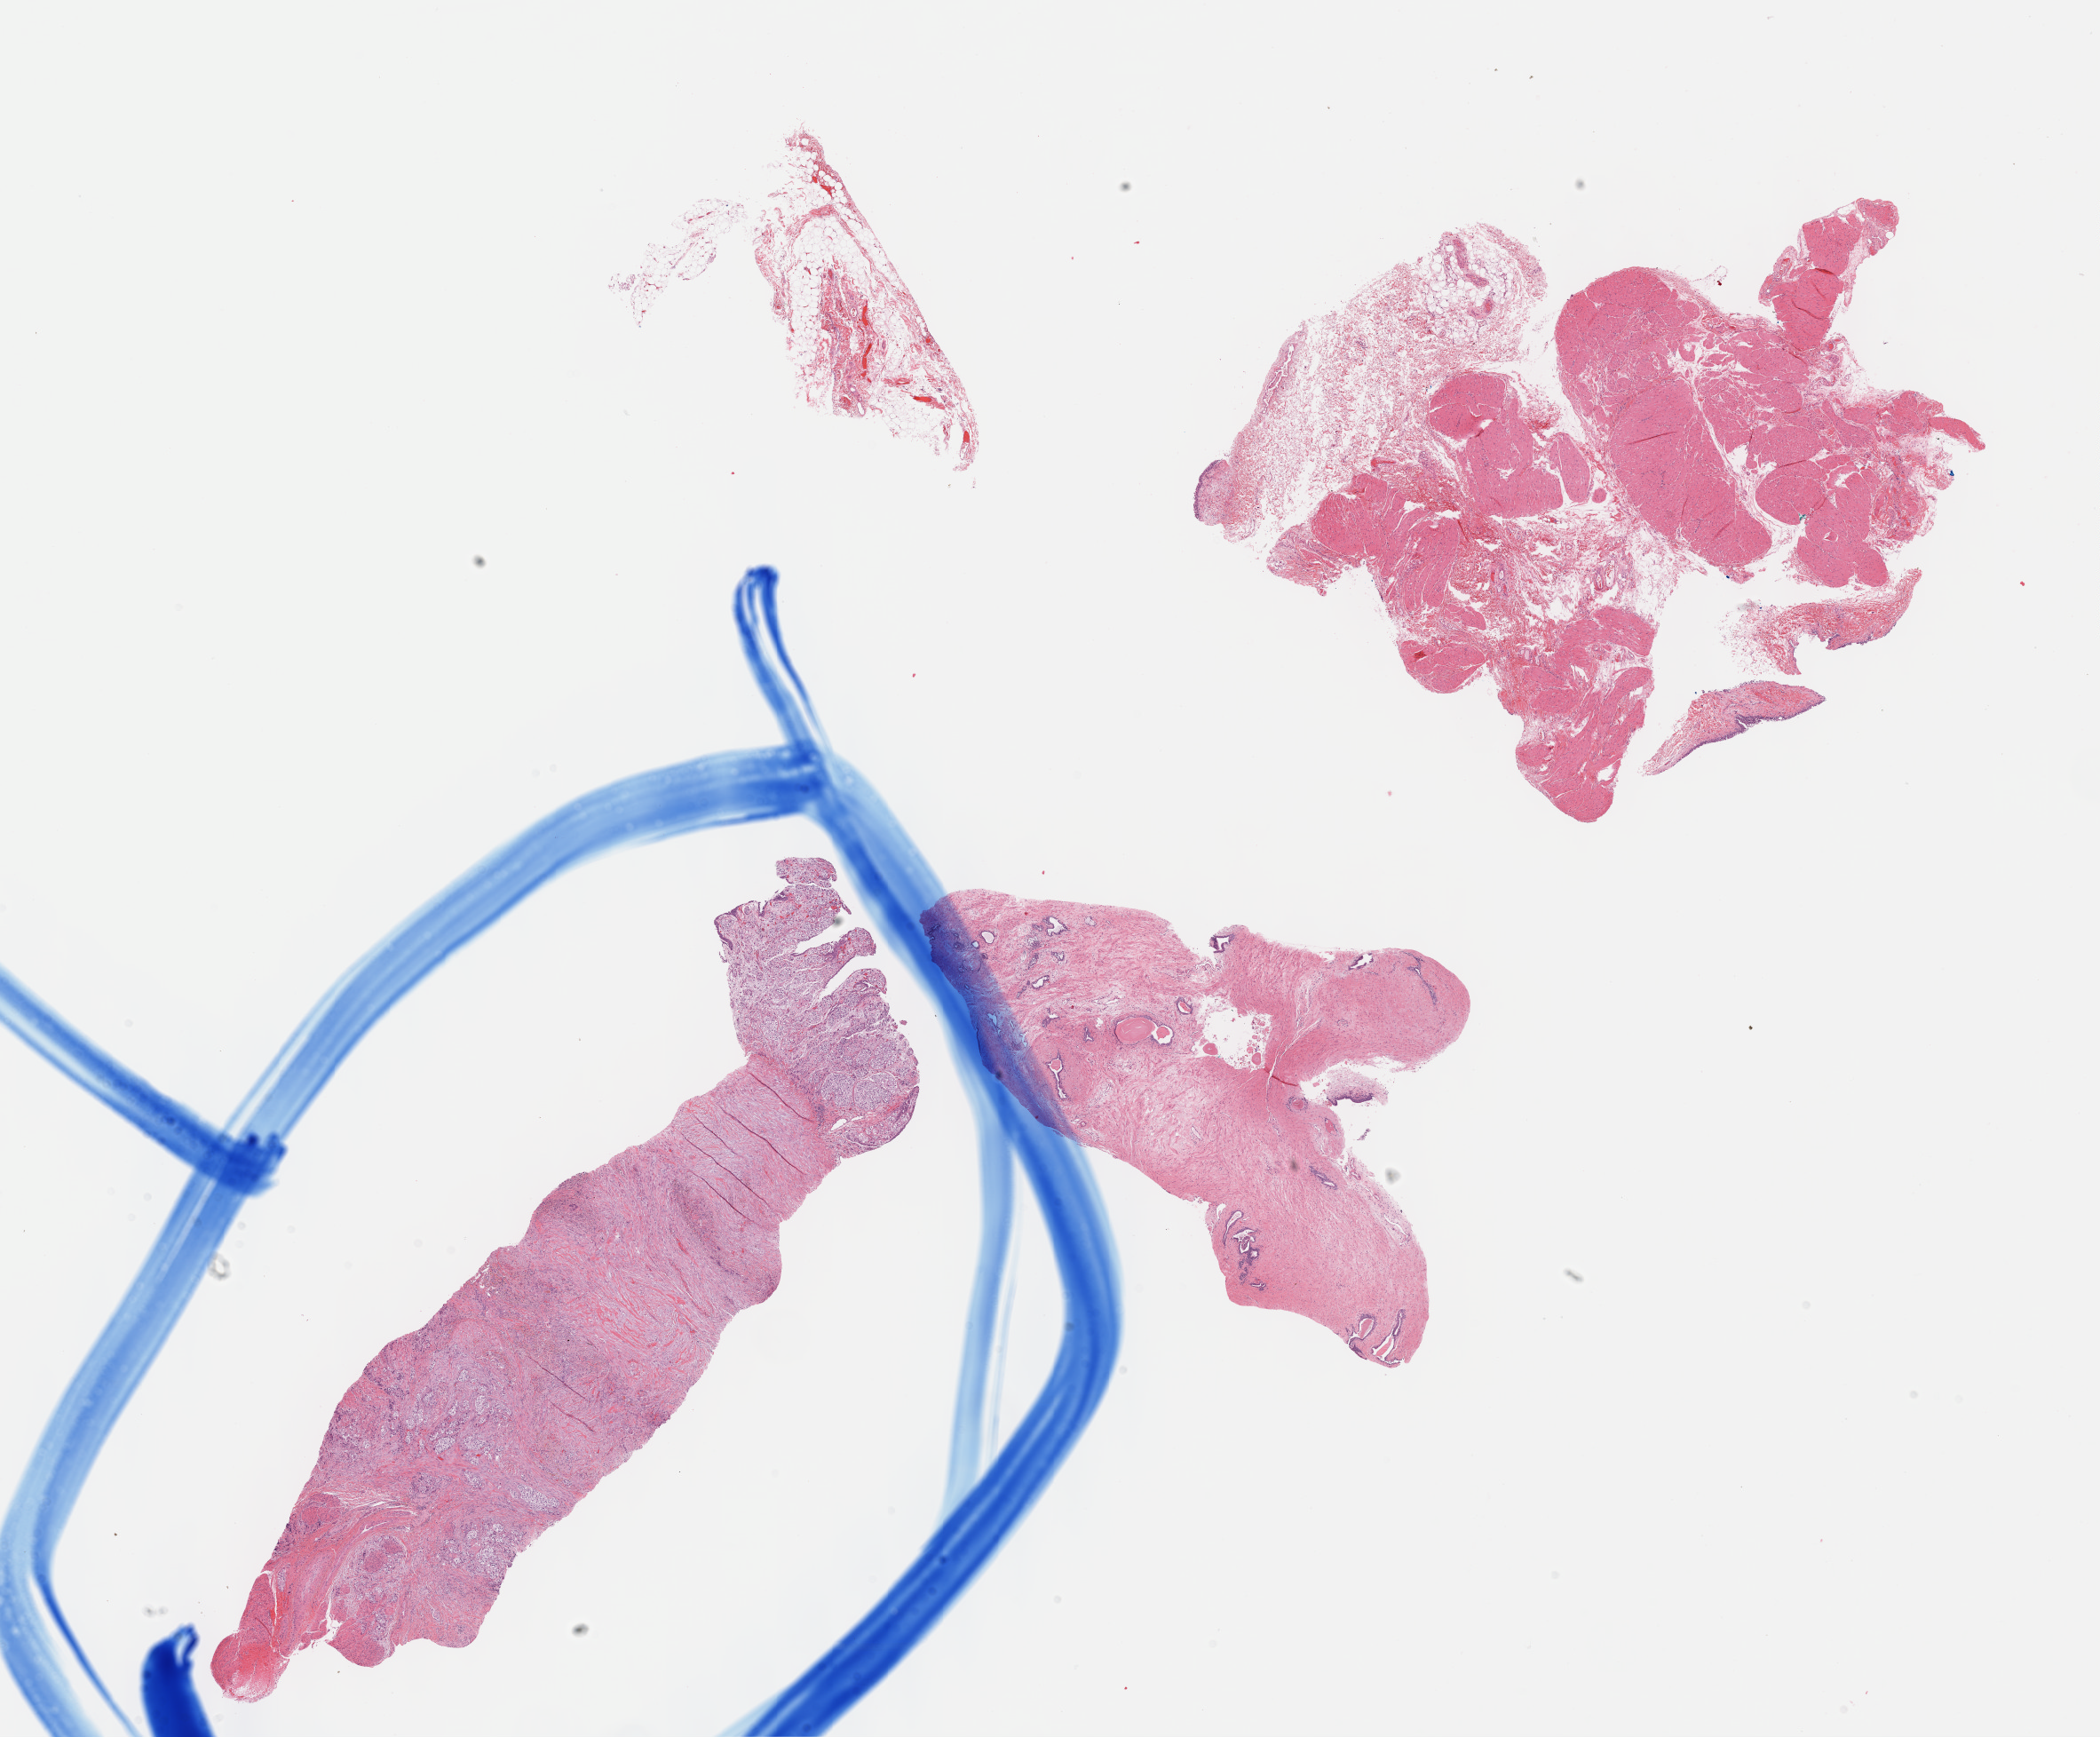
Hematoxylin and eosin (H&E) stained whole-slide image, shown as a low-resolution overview of the whole scanned area (about 19.1 x 15.8 mm); formalin-fixed paraffin-embedded (FFPE) diagnostic section; primary tumour sample from the bladder. Male, age 82 years at initial diagnosis. Histologic grade: high grade.
Lymph nodes positive (case pathology): 1 of 7 examined. Pathologic diagnosis: Transitional cell carcinoma (posterior wall of bladder). AJCC pathologic stage: IV (7th edition).